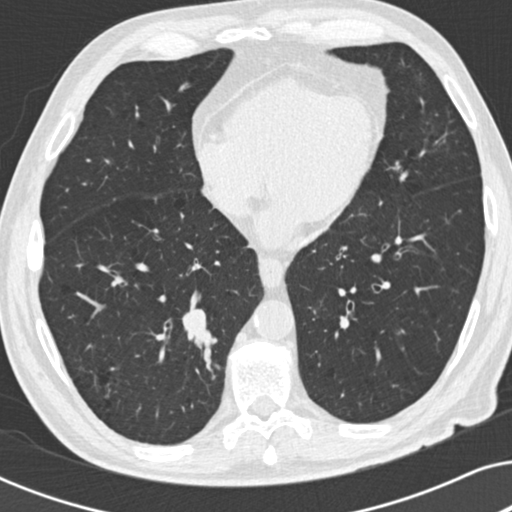
Chest CT (low-dose screening protocol), one axial image. Baseline screening round. Lung window (W 1500 / L -600 HU). Slice 107 of 191 in the series. 512 × 512 image matrix, field of view 330 × 330 mm. Male participant, aged 73 years at enrolment. Current smoker at enrolment.
Expert reader's lesion annotation, bounding box <161,298,224,362> (left, top, right, bottom; pixels). The screening reader recorded 2 non-calcified nodules or masses ≥4 mm on this exam (right lower lobe, right upper lobe); which of them this box marks is not recorded. Official screen result: positive, change unspecified: nodule(s) >= 4 mm or enlarging nodule(s), mass(es), or other non-specific abnormalities suspicious for lung cancer.